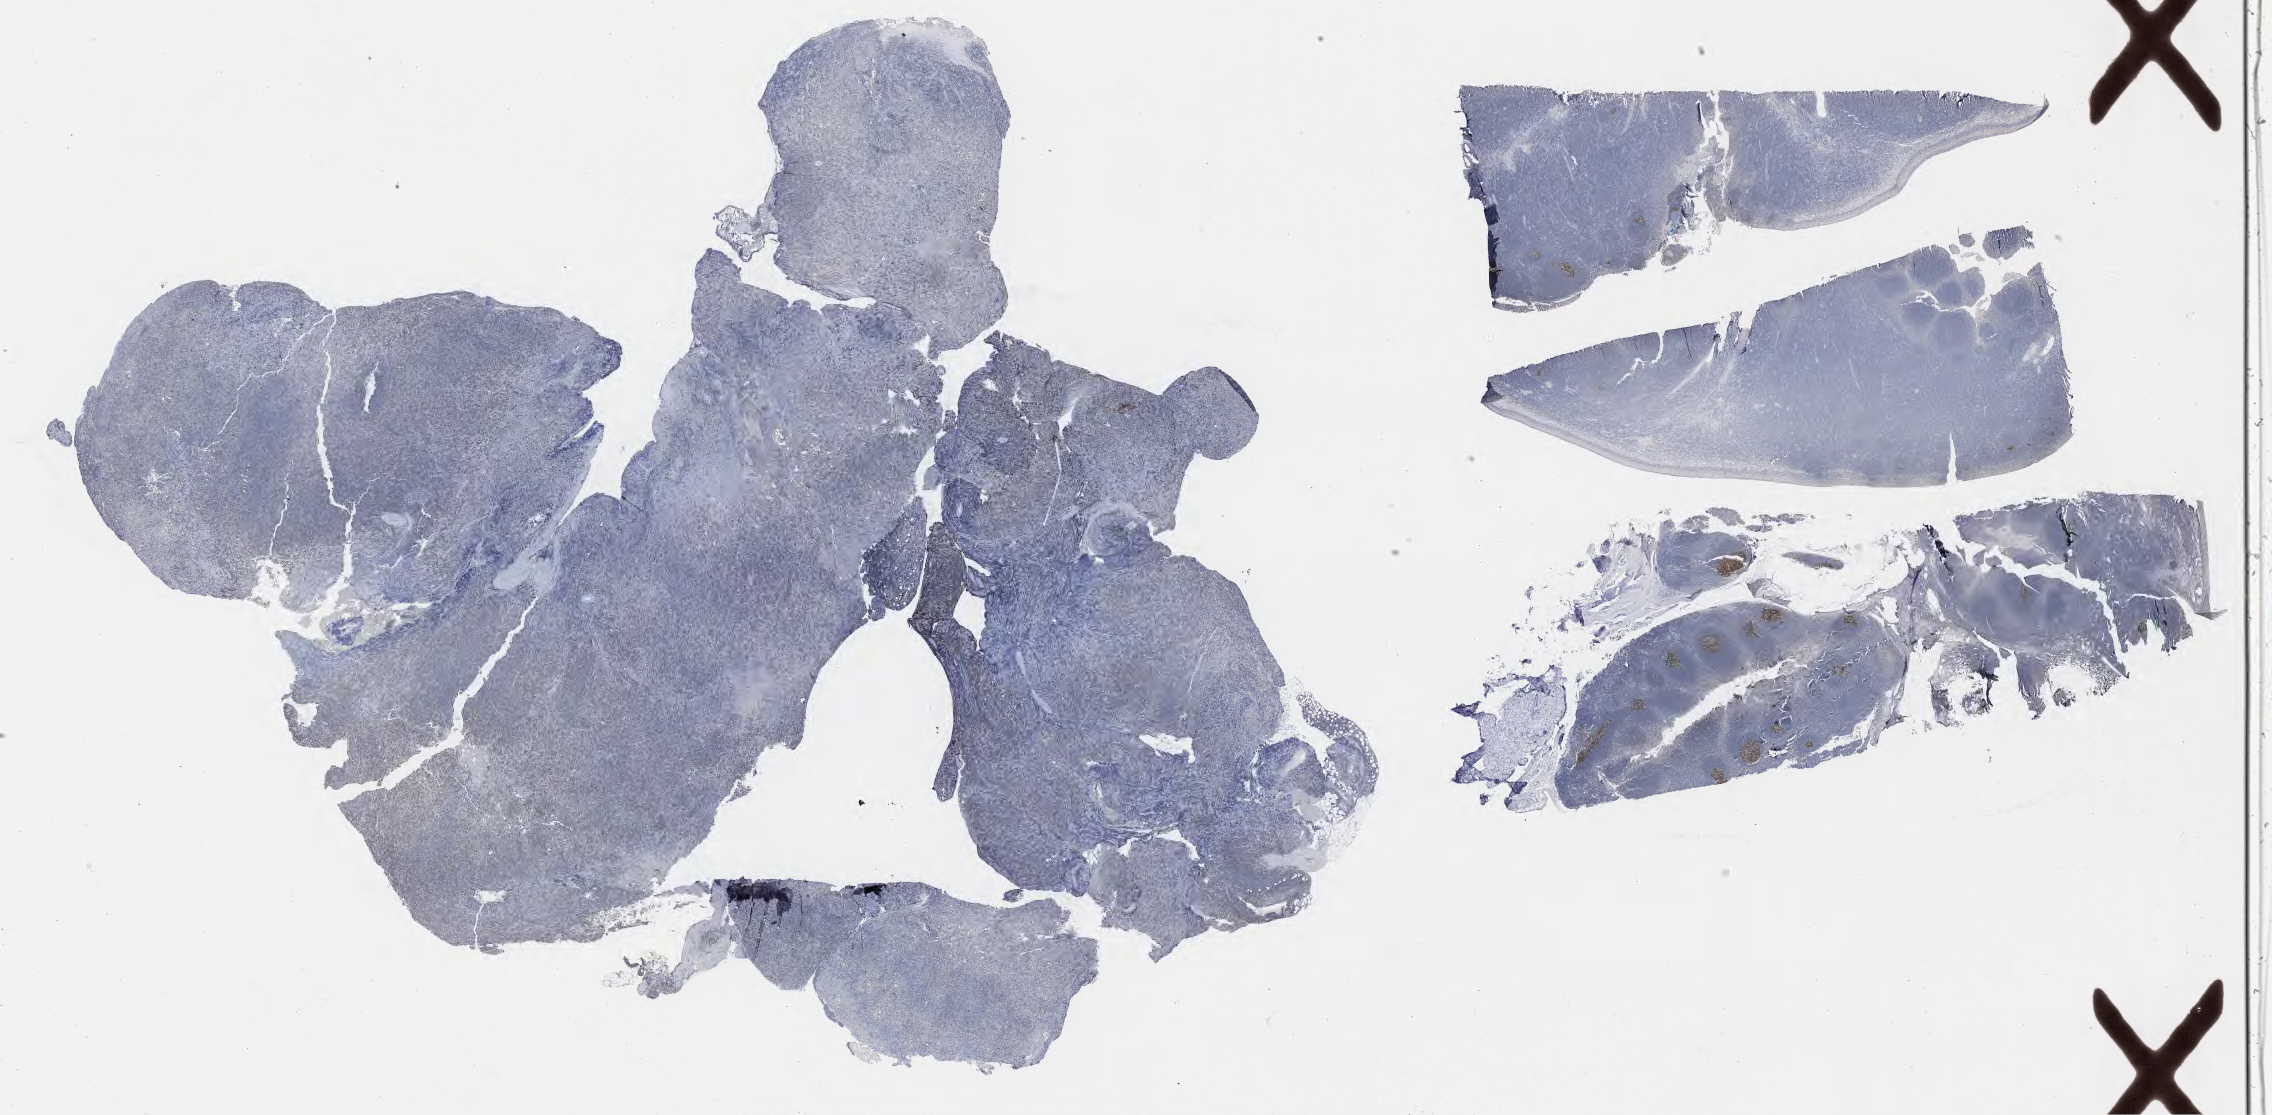
Whole-slide image, immunohistochemical stain for BCL6, shown as a low-resolution overview of the whole scanned area (about 36.7 x 18.0 mm). Specimen: tumor tissue. Anatomic site: soft tissue of abdomen. Patient: female, age at initial diagnosis 8 years.
- histologic diagnosis: Burkitt lymphoma, NOS